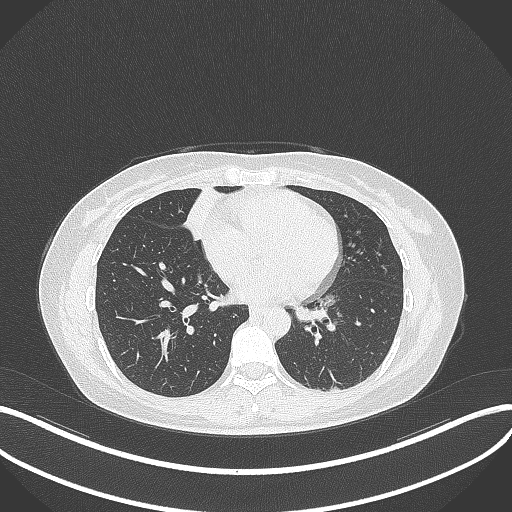
Chest CT, one axial slice. Position 111 of 284 along the scan axis. 120 kVp. Lung window (W 1500 / L -600 HU). 1 mm slice thickness. 512 × 512 image matrix, field of view 400 × 400 mm. Patient: female, 43 years. From the clinical record (not read from this slice): clinical TNM (as recorded): T1c N3 M1; histopathological grade: G1.
Structures marked on this image (bounding box drawn by a radiologist):
- lung tumour (recorded histology: adenocarcinoma): bounding box (x1, y1, x2, y2) in pixels: (185, 184, 225, 240)